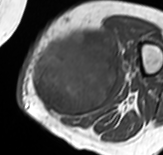
MRI of an extremity soft-tissue mass, one axial slice; position 27 of 65 along the scan axis; MR volume resampled by the dataset authors to the PET/CT grid (not the native acquisition matrix); 3.27 mm slice thickness; 163 × 155 image matrix, field of view 159 × 151 mm. Female patient. From the clinical record (not read from this slice): histological type: pleomorphic leiomyosarcoma; grade: high; site of the primary tumour: left thigh.
Outlined on this slice (expert contour drawn on MRI and transferred to this co-registered scan by the dataset authors):
- gross tumour volume including surrounding oedema: bounding box [x1, y1, x2, y2] px = [32, 29, 120, 118]
- gross tumour volume (mass): [32, 31, 118, 118]